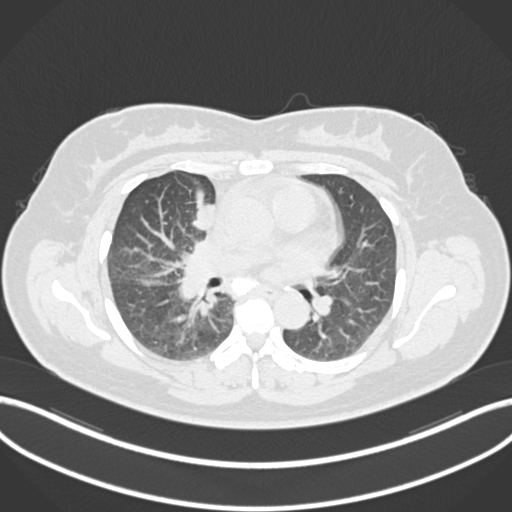
Chest CT, one axial slice; slice 92 of 183 in the series (ordered by position); reconstruction kernel B30f; lung window (W 1500 / L -600 HU); 512 × 512 image matrix, field of view 400 × 400 mm. Female patient, age 46 years. From the clinical record (not read from this slice): clinical TNM (as recorded): T2a N1 M0.
Annotated regions visible in this slice (rectangle marked by the reading radiologist):
- lung tumour (recorded histology: adenocarcinoma): bounding box (x1, y1, x2, y2) in pixels: (190, 197, 224, 238)